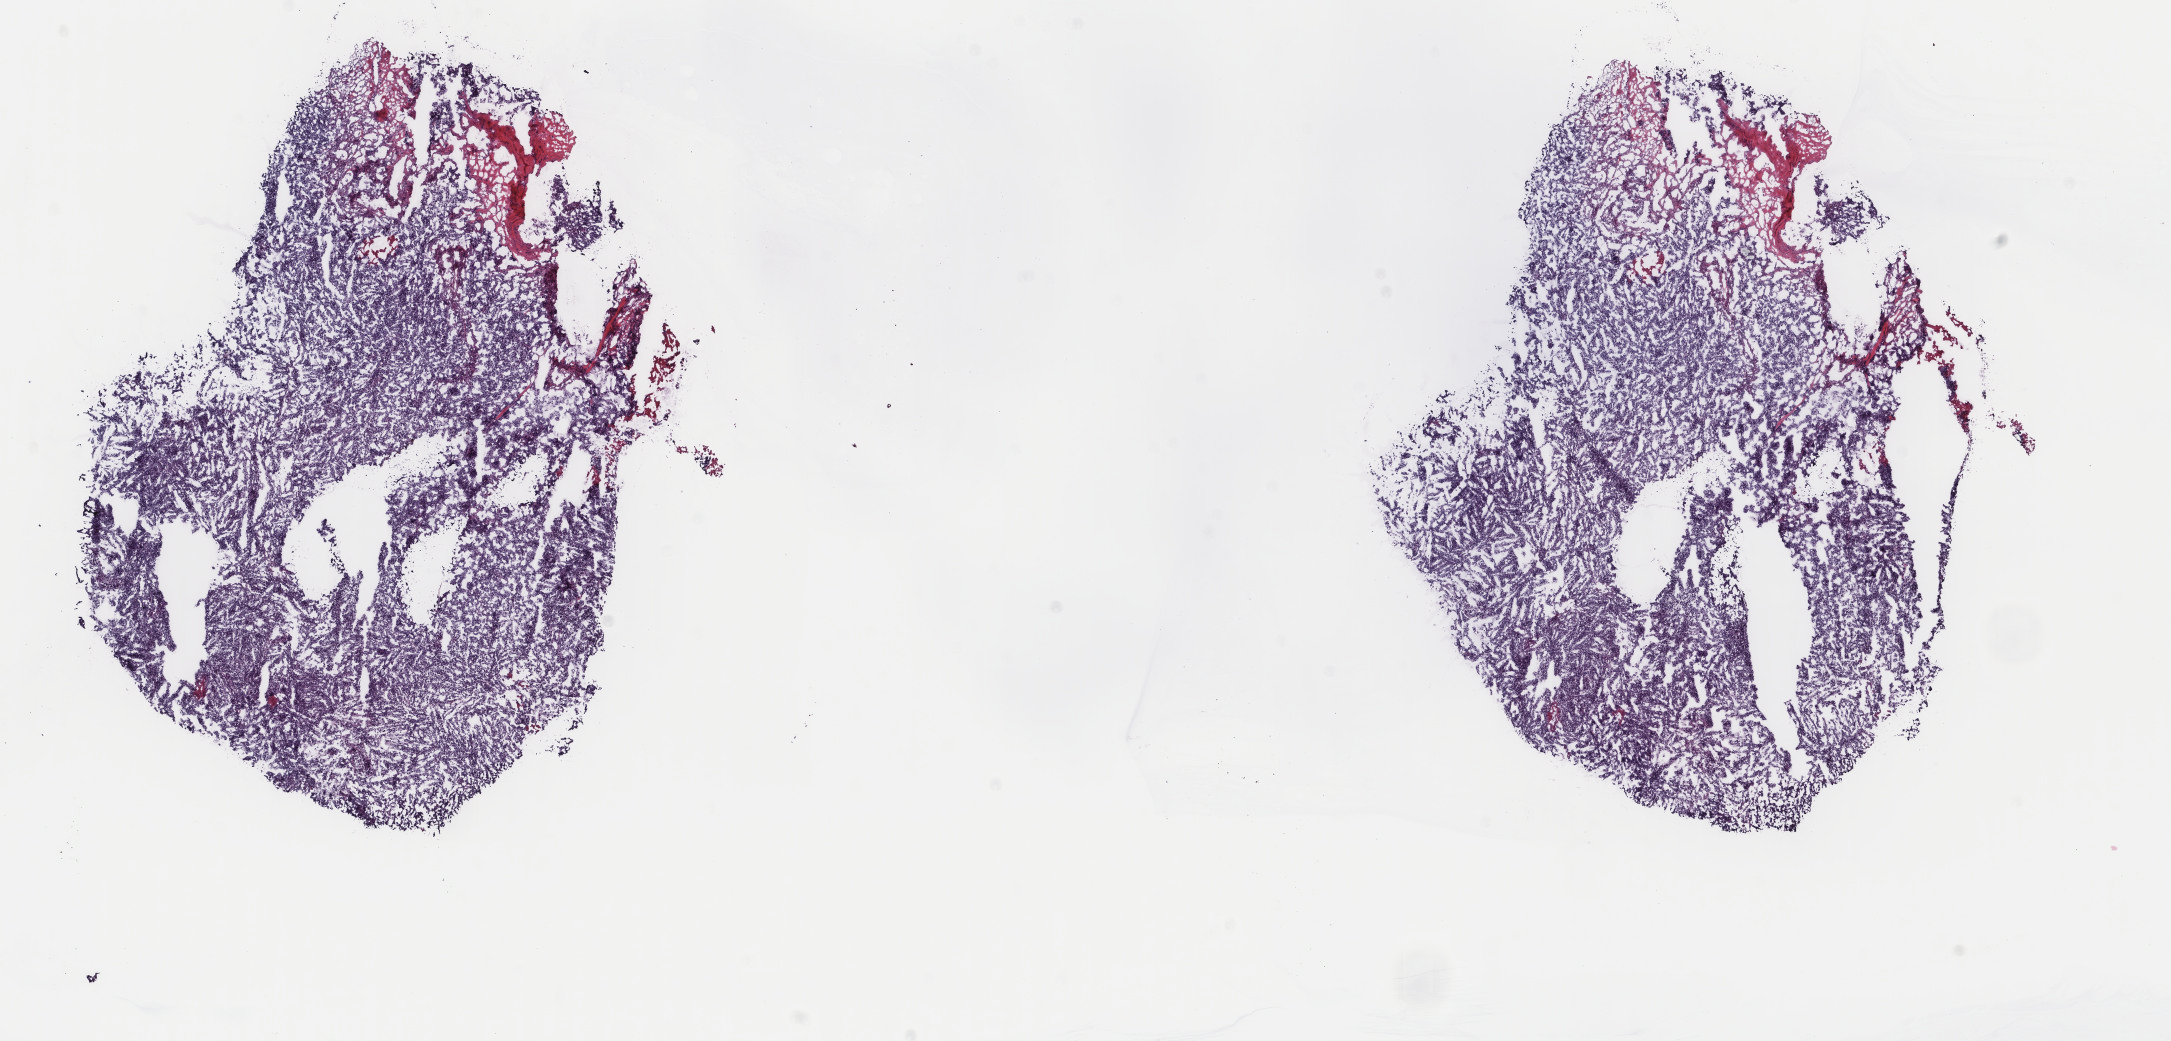
H&E whole-slide image — whole scanned area (about 17.2 x 8.3 mm, acquisition: 40x scan) shown as a low-resolution overview; frozen section from the top of the tissue portion; metastatic tumour sample. Male patient; age at initial diagnosis 71 years. Pathologist review of this section (percent, as recorded): tumour cells 100%, tumour nuclei 97%, normal cells 0%, stromal cells 0%, necrosis 0%. Infiltration values recorded for this section: lymphocyte infiltration 0%, monocyte infiltration 0%, neutrophil infiltration 0%.
This section: metastatic tumour tissue. Patient diagnosis: Malignant melanoma, NOS.